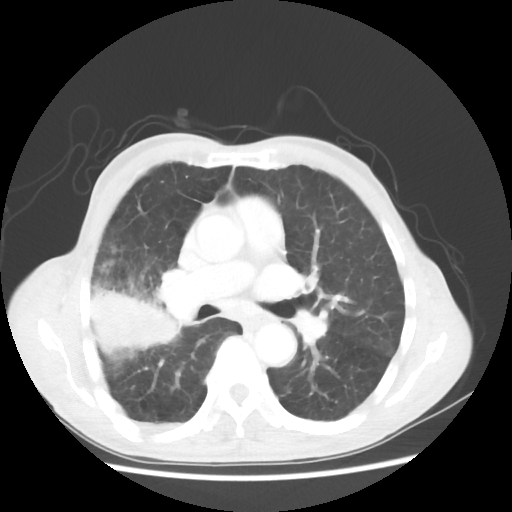
Chest CT, one axial slice. Slice 31 of 58 in the series (ordered by position). 100 kVp. Lung window (W 1500 / L -600 HU). 5 mm slice thickness. 512 × 512 image matrix. Patient: male, 75 years. From the clinical record (not read from this slice): clinical TNM (as recorded): T4 N1 M1.
Structures marked on this image (bounding box drawn by a radiologist):
- lung tumour (recorded histology: adenocarcinoma): bounding box (x1, y1, x2, y2) in pixels: (85, 277, 184, 360)